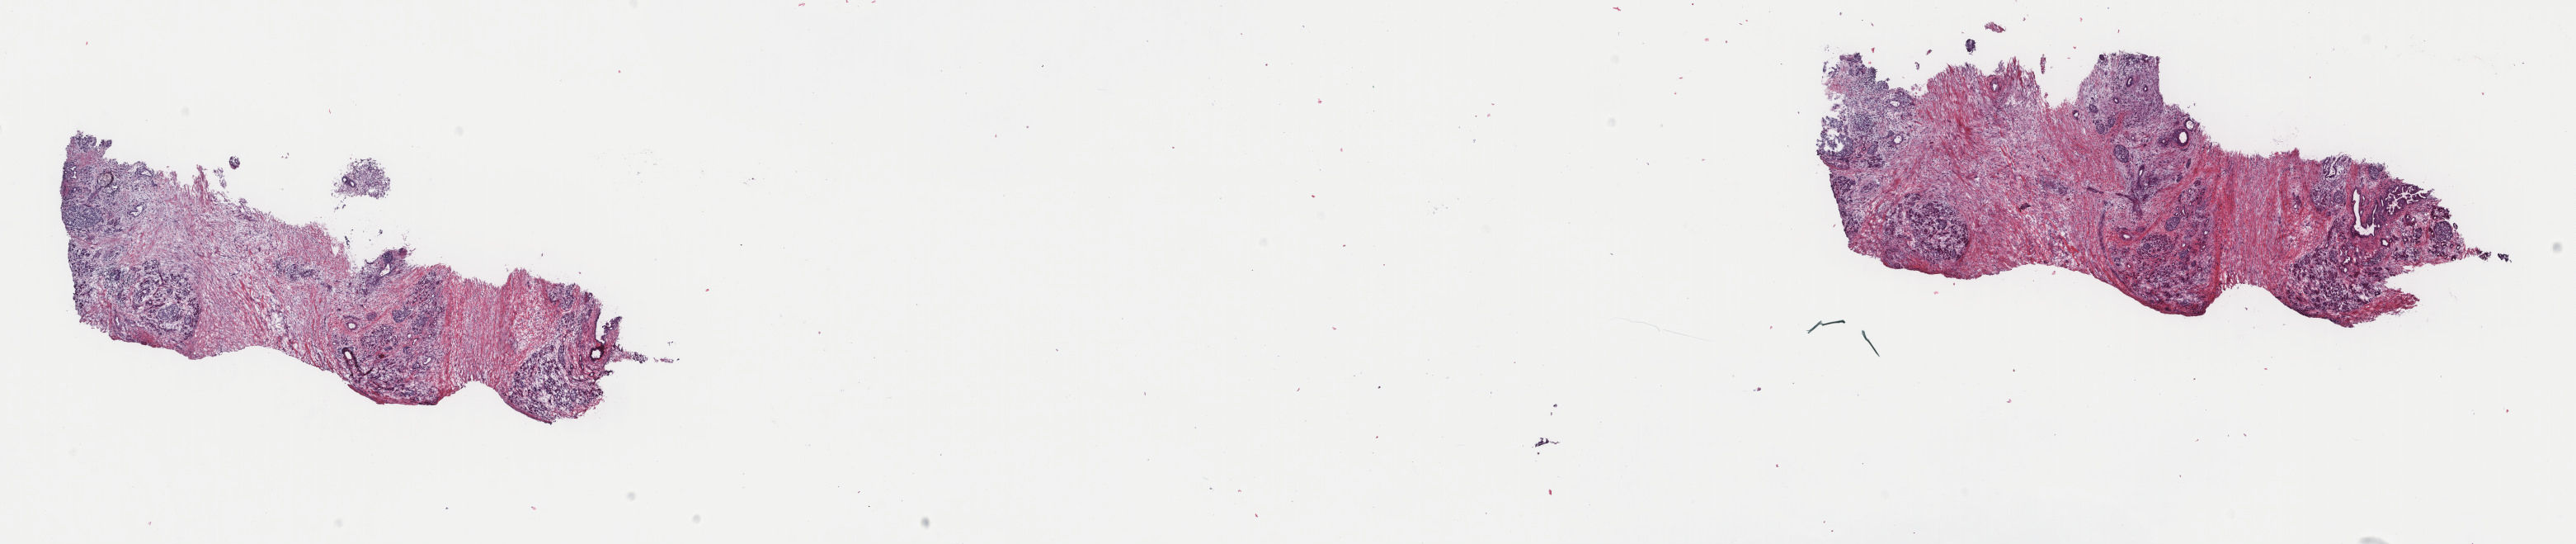
Whole-slide histology image, H&E-stained — a low-resolution overview of the entire scanned area, about 24.8 x 5.2 mm, frozen section, sample: primary tumour, pancreas. Female patient. Histologic grade: G3 (poorly differentiated). Pathologist review of this section (percent, as recorded): tumour cells 20%, tumour nuclei 10%, normal cells 80%, stromal cells 0%, necrosis 0%. Infiltration values recorded for this section: lymphocyte infiltration 2%, monocyte infiltration 0%, neutrophil infiltration 0%.
• AJCC pathologic stage: IIB (7th edition)
• TNM: T3 N1 MX
• lymph nodes positive (case pathology): 1 of 12 examined
• diagnosis: Adenocarcinoma, NOS (tail of pancreas)